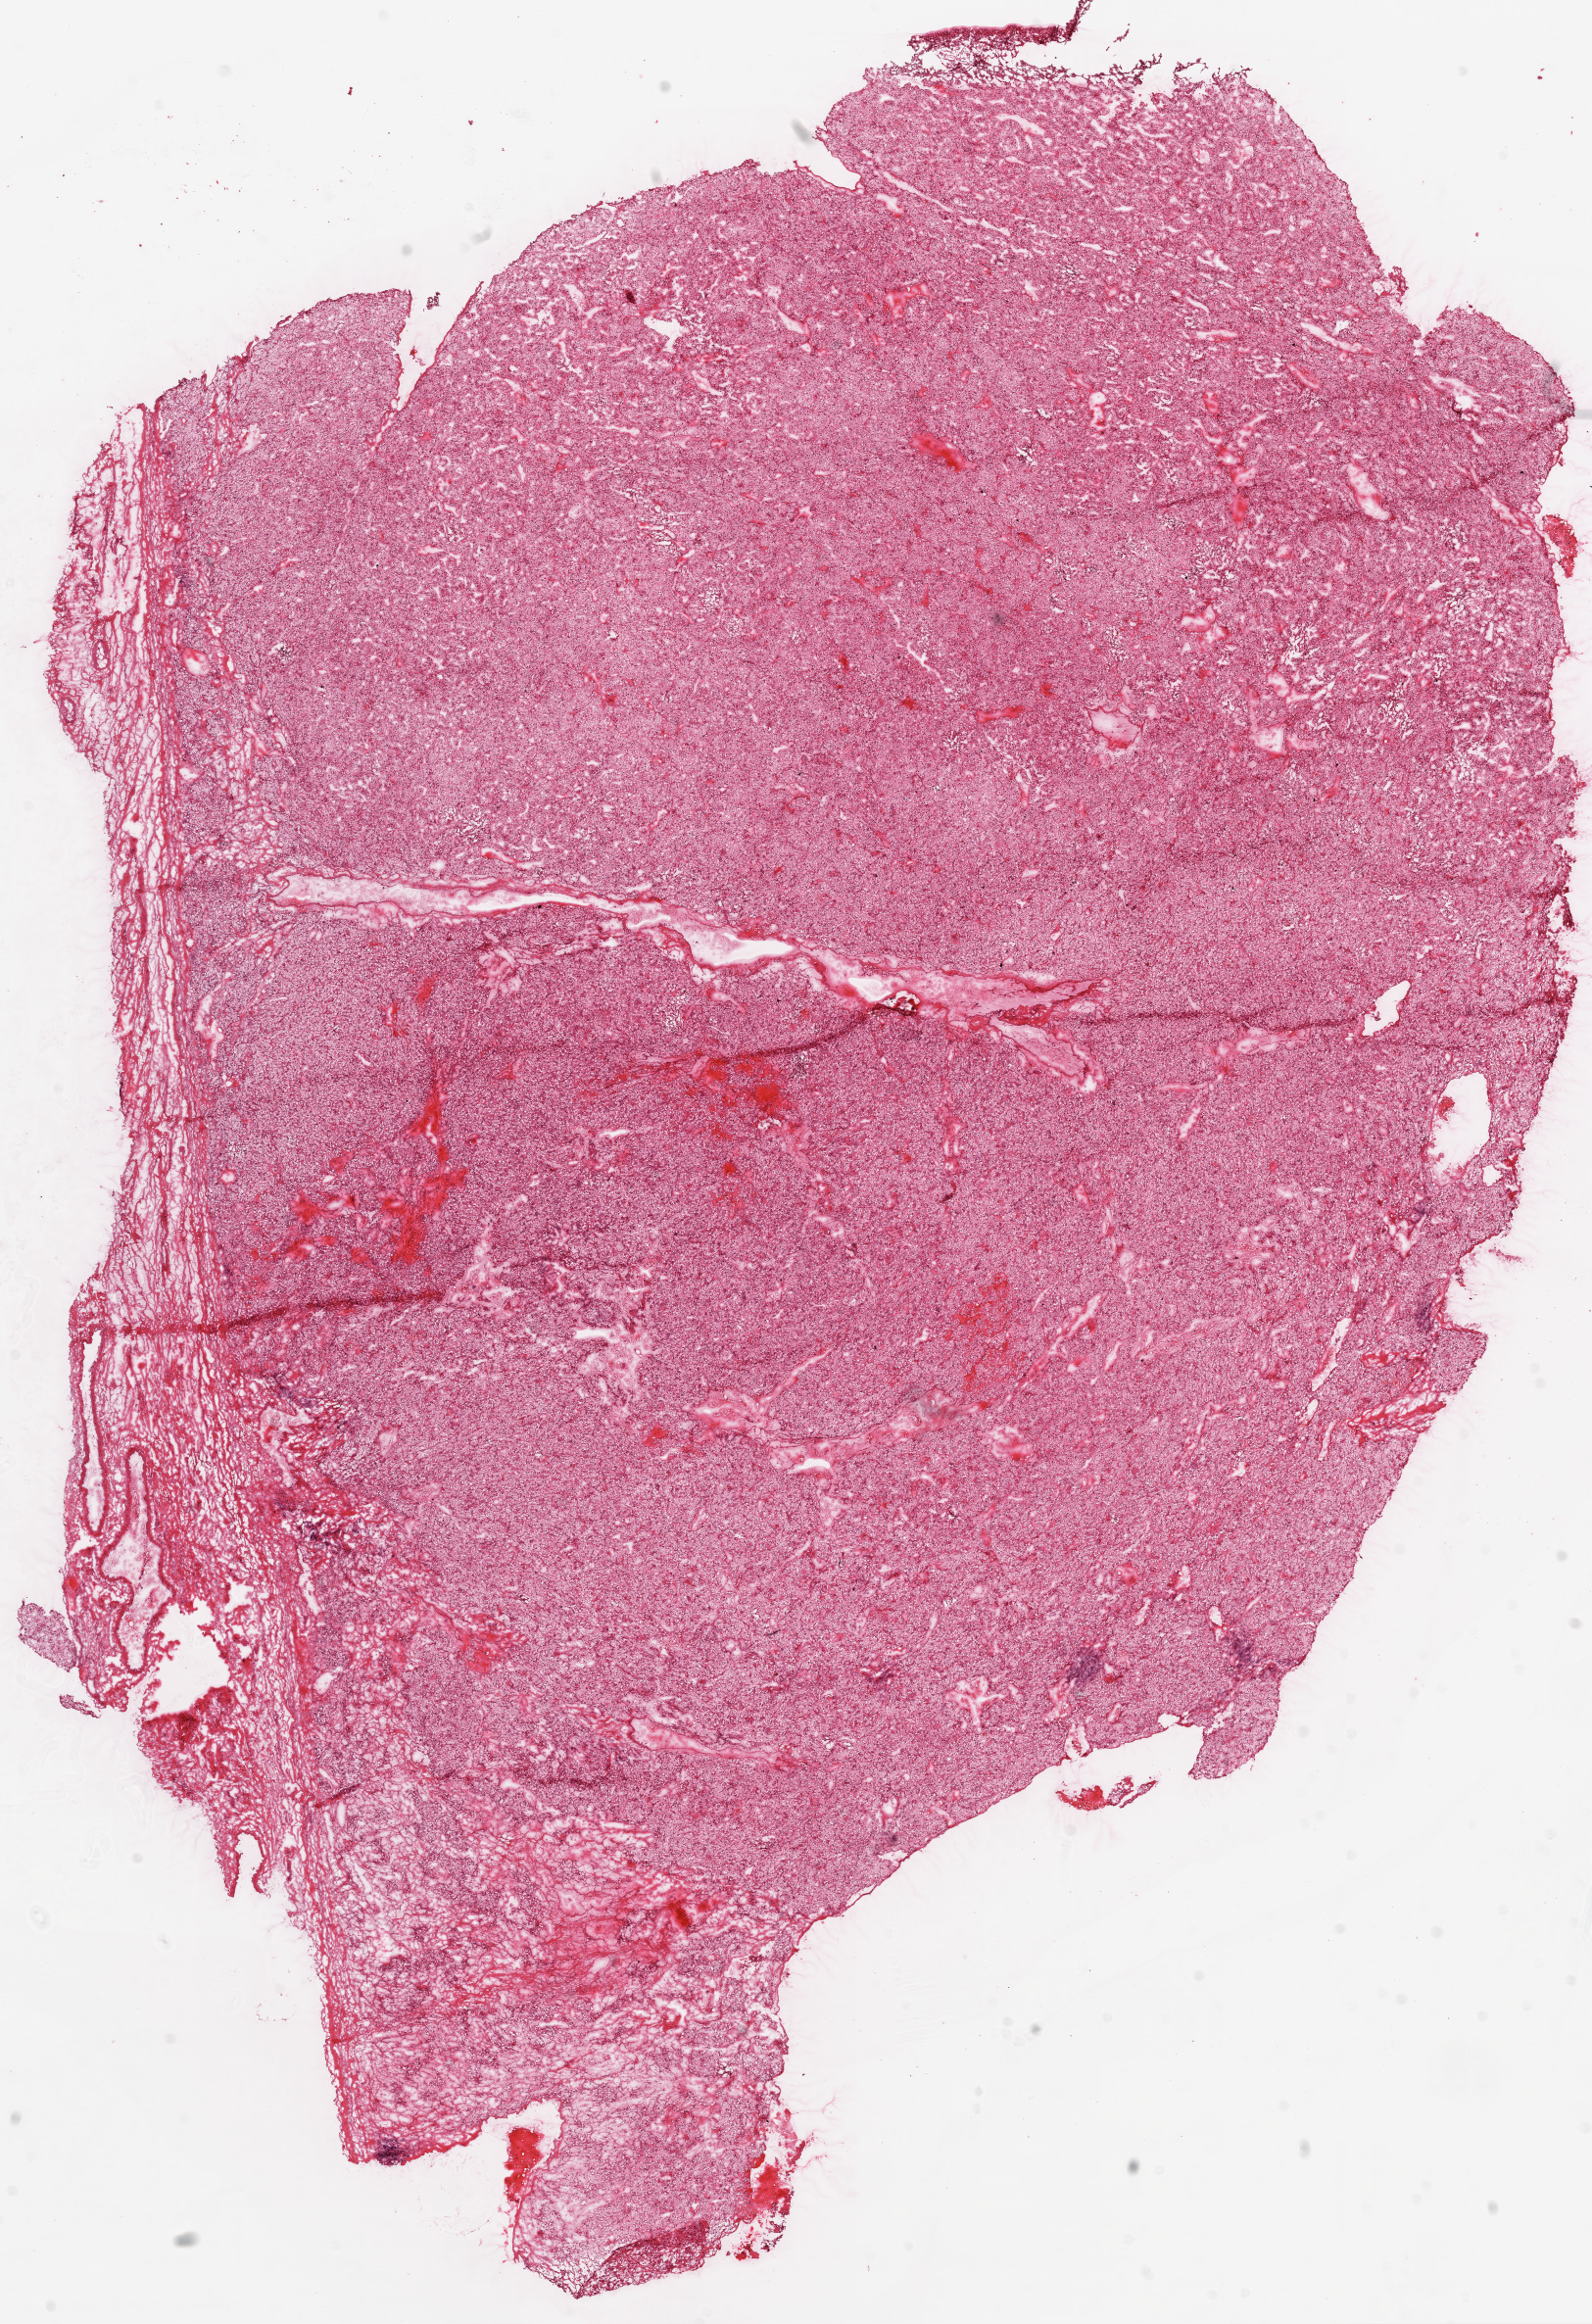
Digitized H&E tissue section (whole slide), shown as a low-resolution overview of the whole scanned area (about 13.0 x 19.0 mm). Frozen section from the top of the tissue portion. Primary tumour sample from the kidney. Female, age 65 years at initial diagnosis. Histologic grade: G2 (moderately differentiated). Slide review estimates, as recorded: tumour cells 95%, tumour nuclei 90%, normal cells 0%, stromal cells 5%, necrosis 0%.
Diagnosis: Clear cell adenocarcinoma, NOS. Laterality: right. AJCC pathologic stage: I.